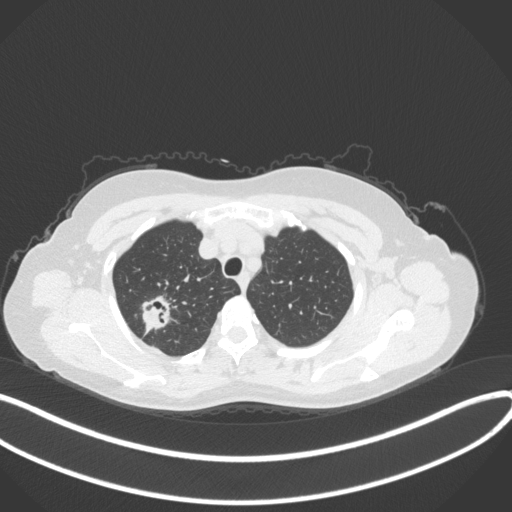
Chest CT, one axial slice. Position 299 of 342 along the scan axis. Lung window (W 1500 / L -600 HU). 1 mm slice thickness. 512 × 512 image matrix, field of view 400 × 400 mm. Female patient, age 50 years. From the clinical record (not read from this slice): clinical TNM (as recorded): T1c N0 M0.
Structures marked on this image (rectangle marked by the reading radiologist):
- lung tumour (recorded histology: adenocarcinoma): box from (x=139, y=291) to (x=175, y=332) px